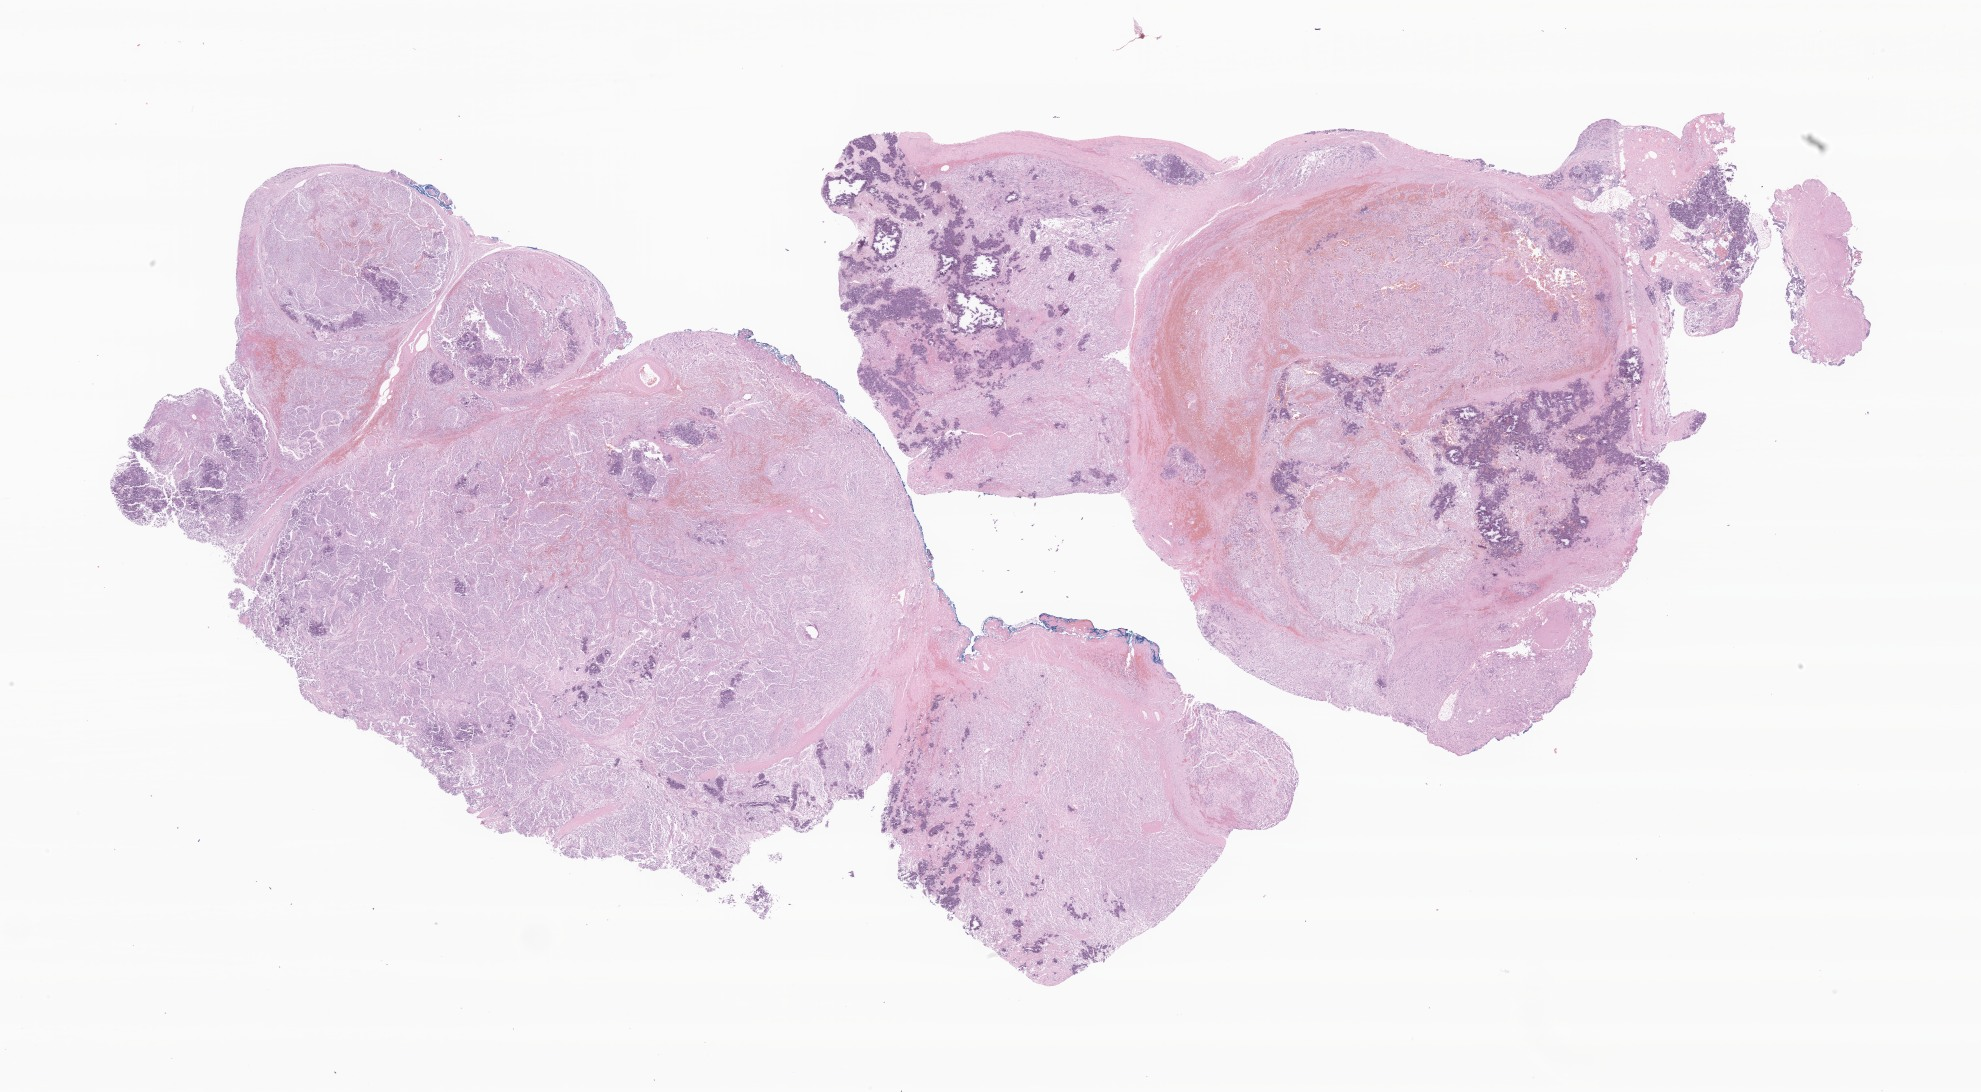
Digitized H&E-stained section of tumor tissue from the spinal cord, shown as a low-resolution overview of the whole scanned area (about 33.4 x 18.4 mm), formalin-fixed paraffin-embedded section. Patient: female, age 347 days.
Diagnosis (ICD-O-3 morphology term): Neuroblastoma, NOS.